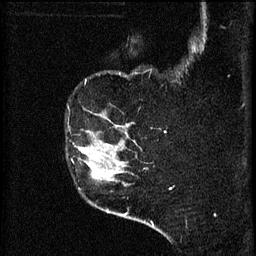
Breast MRI (dynamic contrast-enhanced), one sagittal slice. 3 images stored at this slice position (order not interpretable as contrast timing). 1.5 T. TE 4.2 ms, TR 8.2 ms. 256 × 256 image matrix, field of view 180 × 180 mm. Female patient, age 49 years.
Structures marked on this image (semi-automatic segmentation, software-assisted and operator-edited):
- analysis volume of interest (the breast-tissue region the enhancement analysis was run in; not a lesion): bounding box [x1, y1, x2, y2] px = [76, 132, 105, 177]
- tumour enhancement mask (voxels above the 70 % enhancement threshold inside the analysis volume of interest): [79, 146, 105, 177]